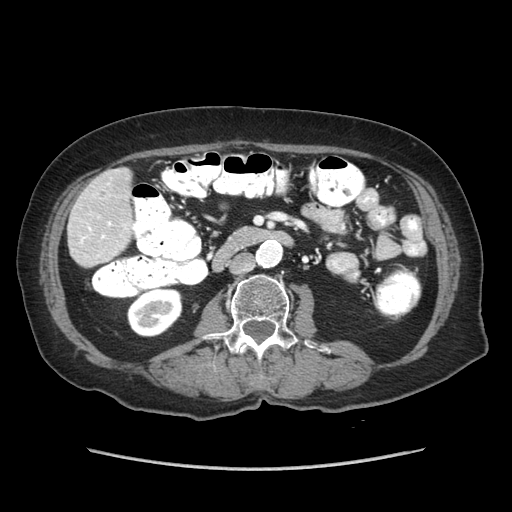
Contrast-enhanced abdominal CT (liver protocol), one axial slice. Slice 14 of 89 in the series (ordered by position). Reconstruction kernel STANDARD. 140 kVp. Soft-tissue window (W 400 / L 40 HU). 2.5 mm slice thickness. 512 × 512 image matrix, field of view 360 × 360 mm. Case-level facts recorded for this patient, not image findings: diagnosis: hepatocellular carcinoma (patient treated with transarterial chemoembolisation; whether this scan precedes or follows treatment is not stated here); TNM stage (as recorded): Stage-IIIA; Child-Pugh class: A; tumour differentiation: well differentiated; tumour size: 11 cm.
Outlined on this slice (semi-automatically segmented with operator editing):
- liver parenchyma outside the tumour (the mass and vessels are separate outlines, so this box may not span the whole liver): bounding box (x1, y1, x2, y2) in pixels: (68, 168, 132, 266)
- liver vessels: (80, 221, 111, 243)